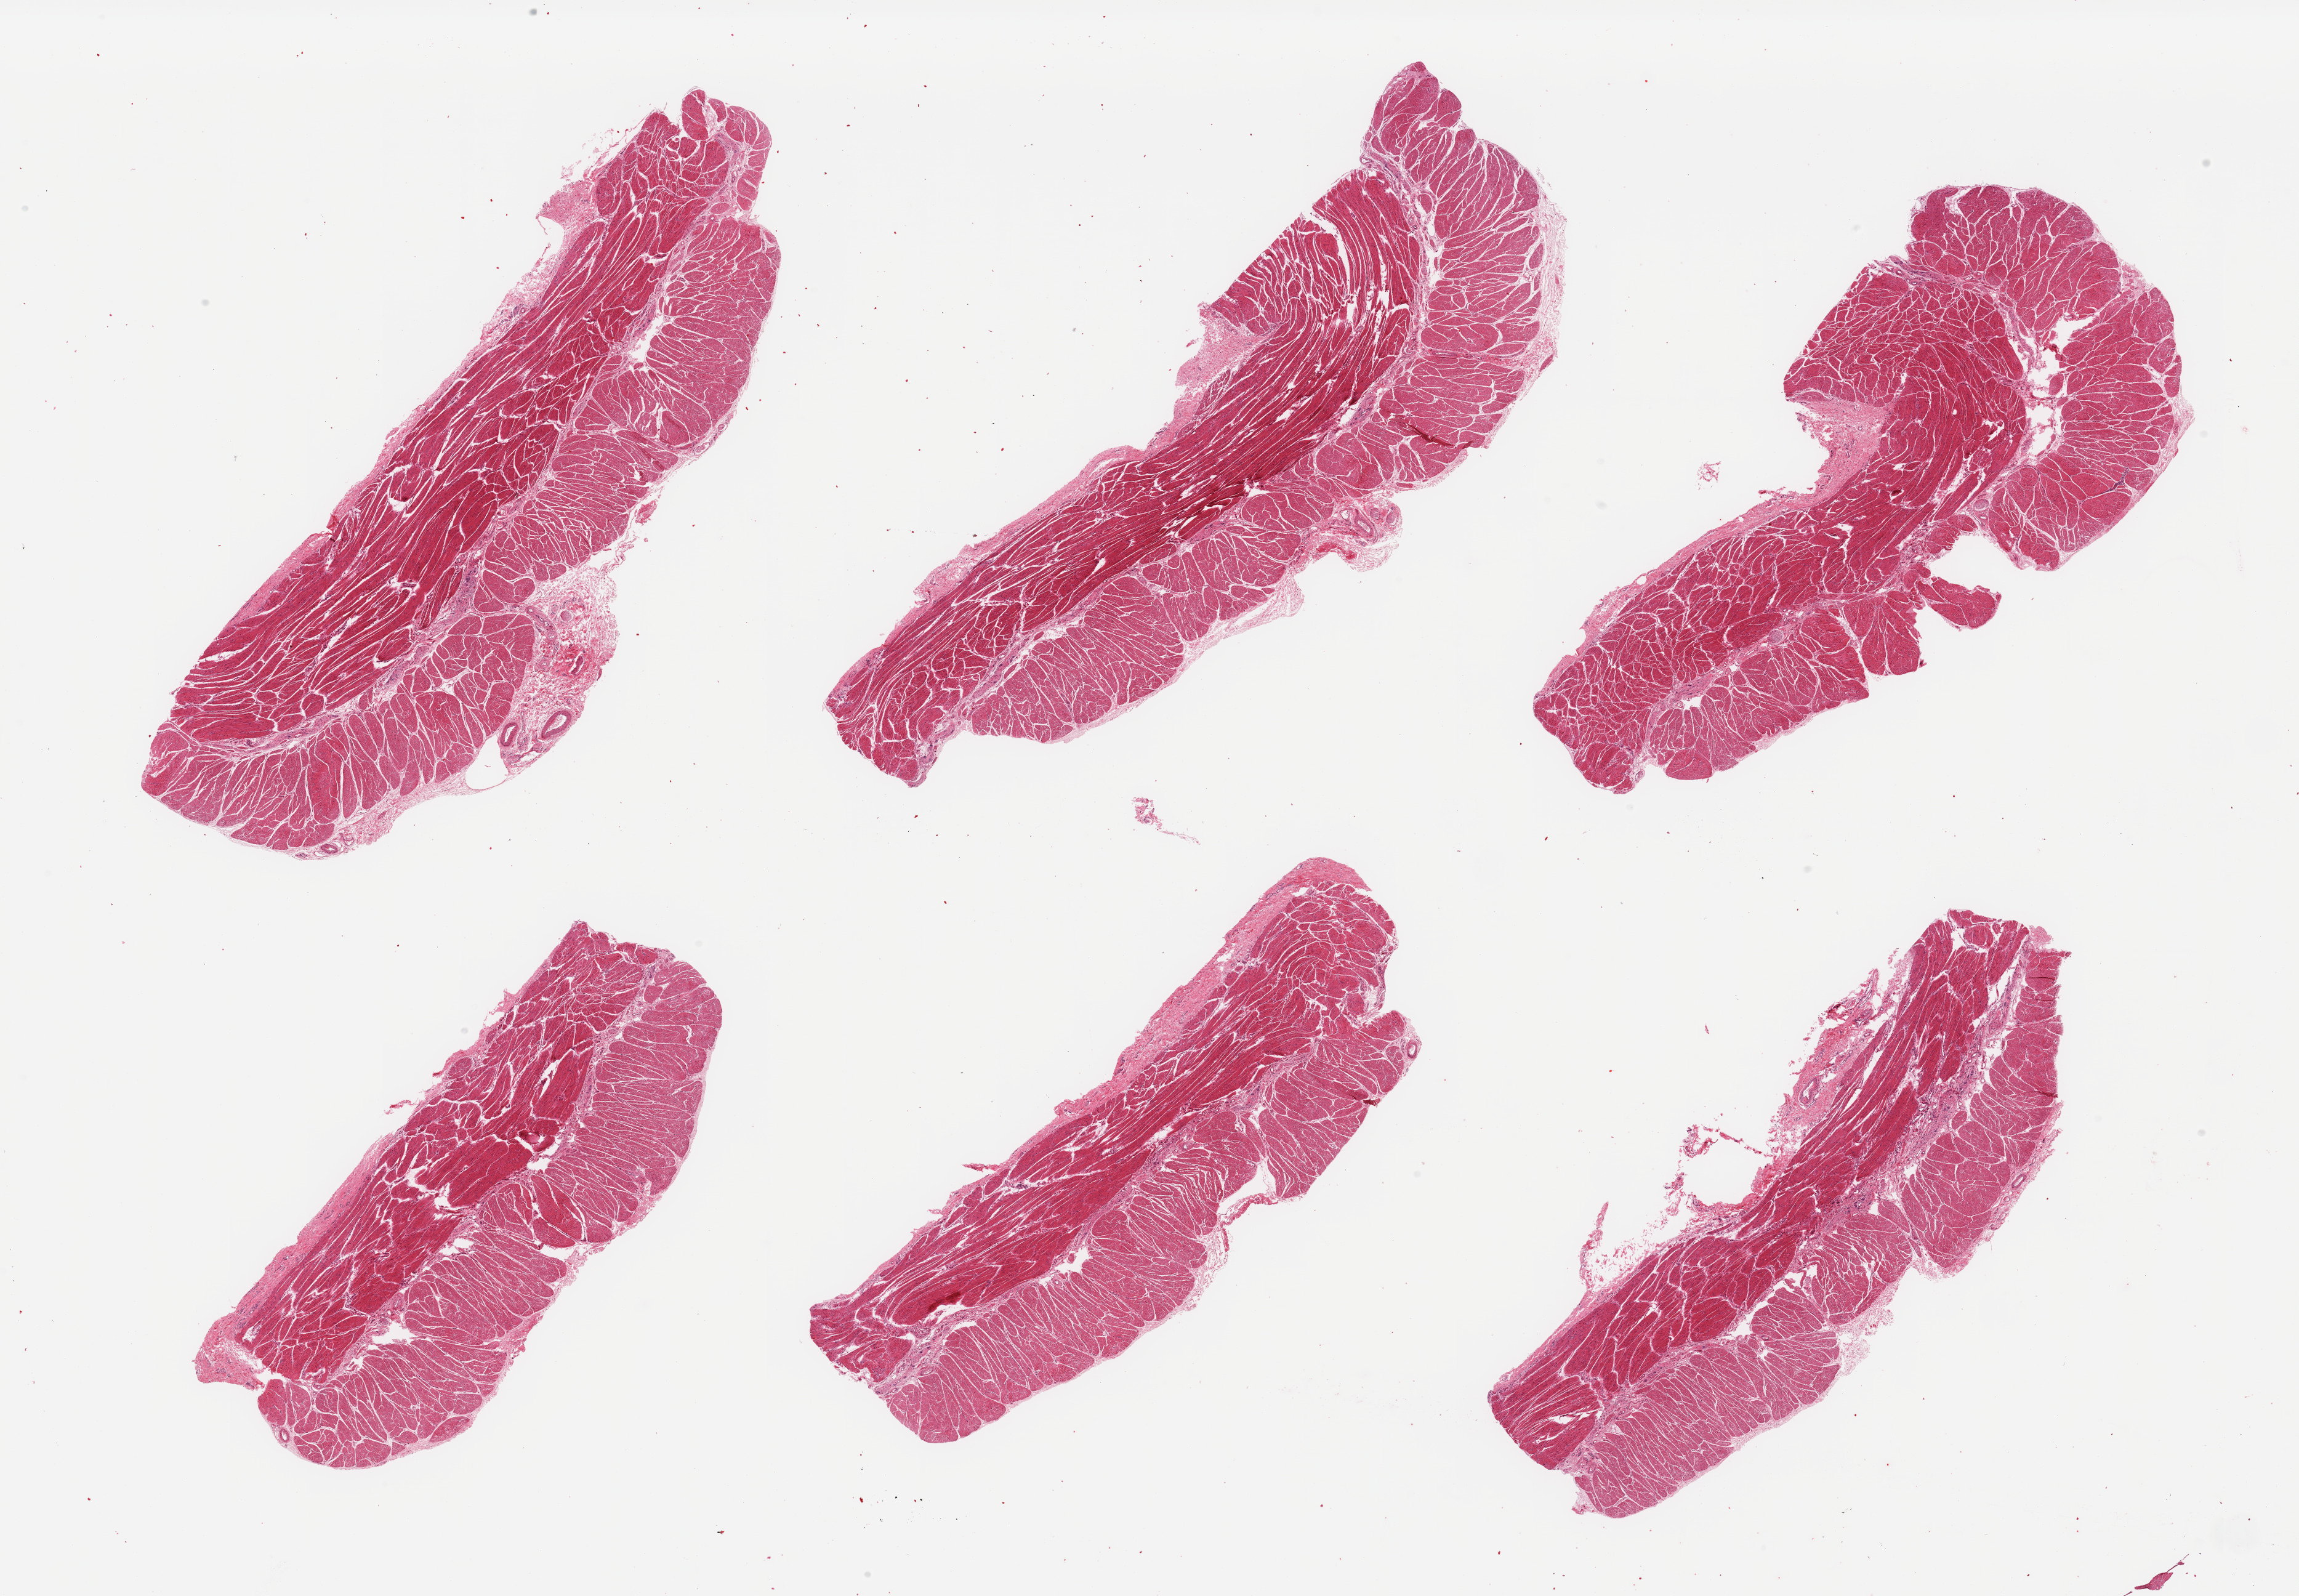
H&E whole-slide image — a low-resolution overview of the entire scanned area, about 29.5 x 20.5 mm, PAXgene-fixed paraffin-embedded (PFPE) section, section of esophageal muscle (target tissue), tissue donor sample. Donor sex: female.
Pathologist's review note for this sample: 6 pieces; target muscularis.